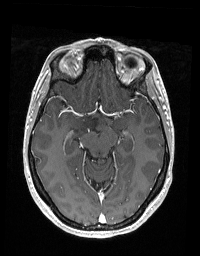
Brain MRI from a brain-tumour surgery series, one axial slice. Position 113 of 192 along the scan axis. T1-weighted post-contrast. 1 mm slice thickness. 200 × 256 image matrix, field of view 195 × 250 mm. Case-level facts recorded for this patient, not image findings: histopathology: Glioblastoma; WHO grade: 2.
Annotated regions visible in this slice (outlined manually by an expert reader):
- tumour: bounding box (x1, y1, x2, y2) in pixels: (74, 116, 97, 136)